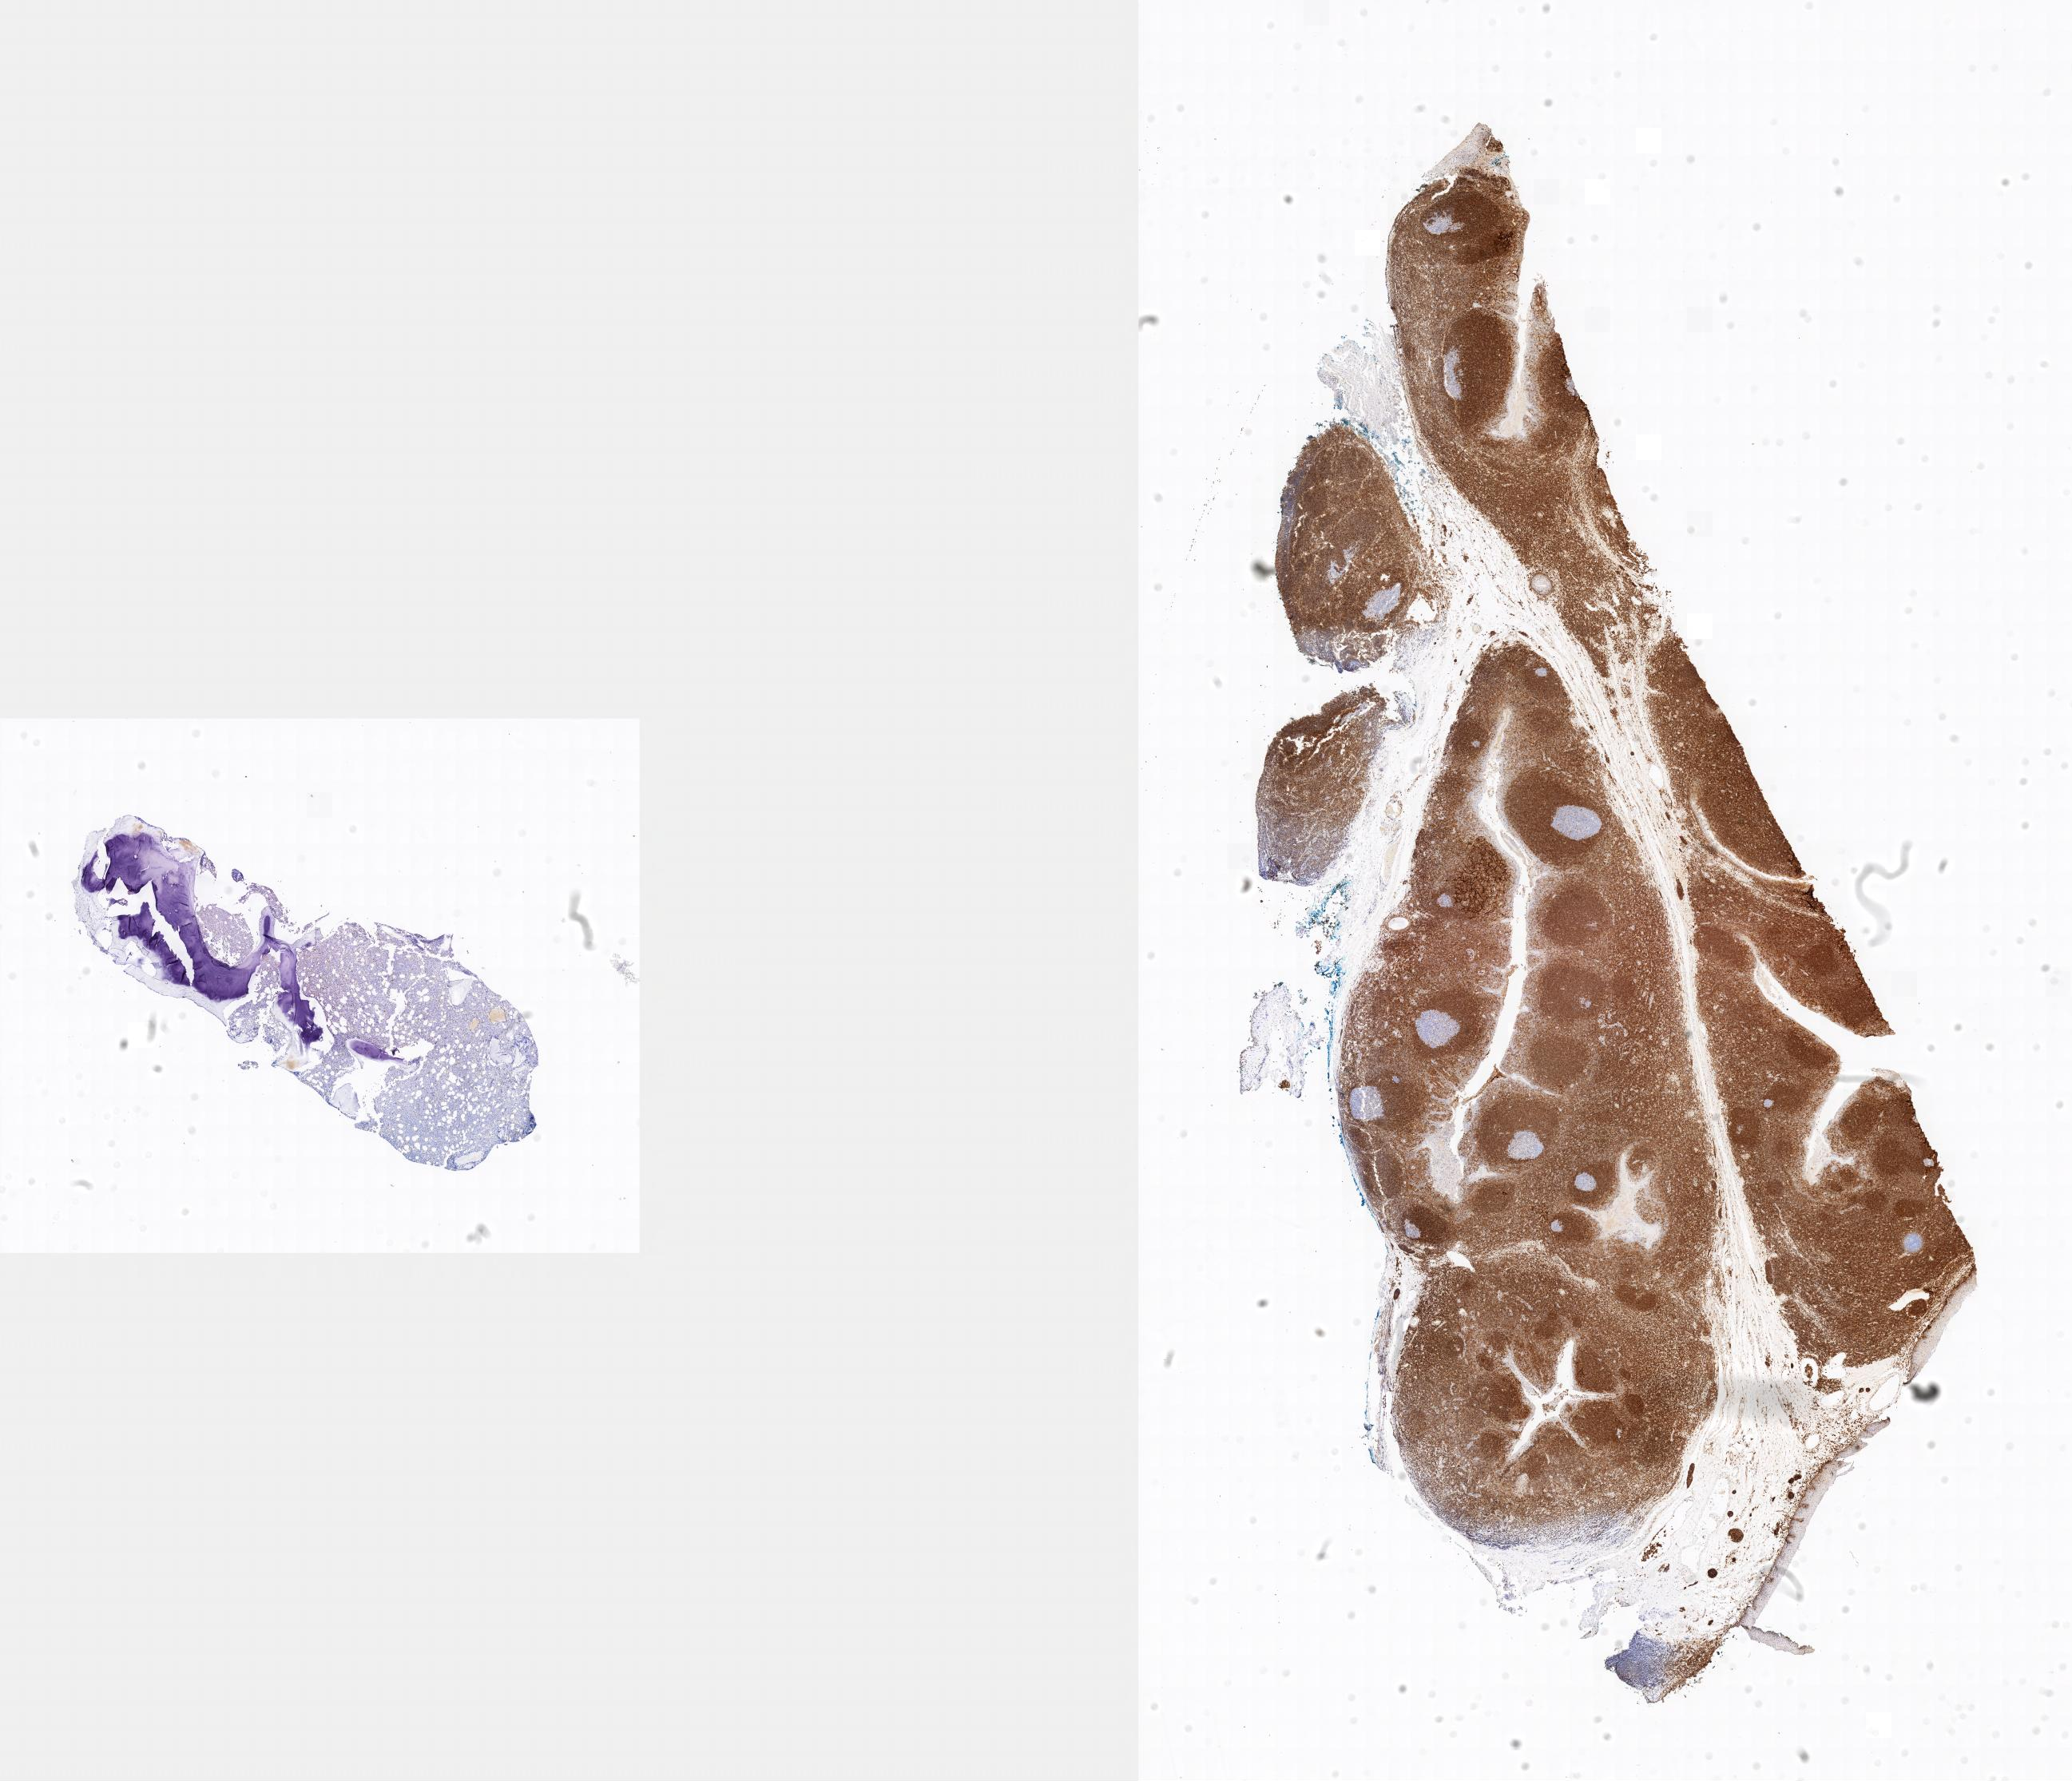
Immunohistochemistry (IHC) whole-slide image stained for BCL2, a low-resolution overview of the entire scanned area; specimen: tumor tissue; anatomic site: bone marrow. Patient: male, 15 years old.
Histologic diagnosis: Burkitt lymphoma, NOS.